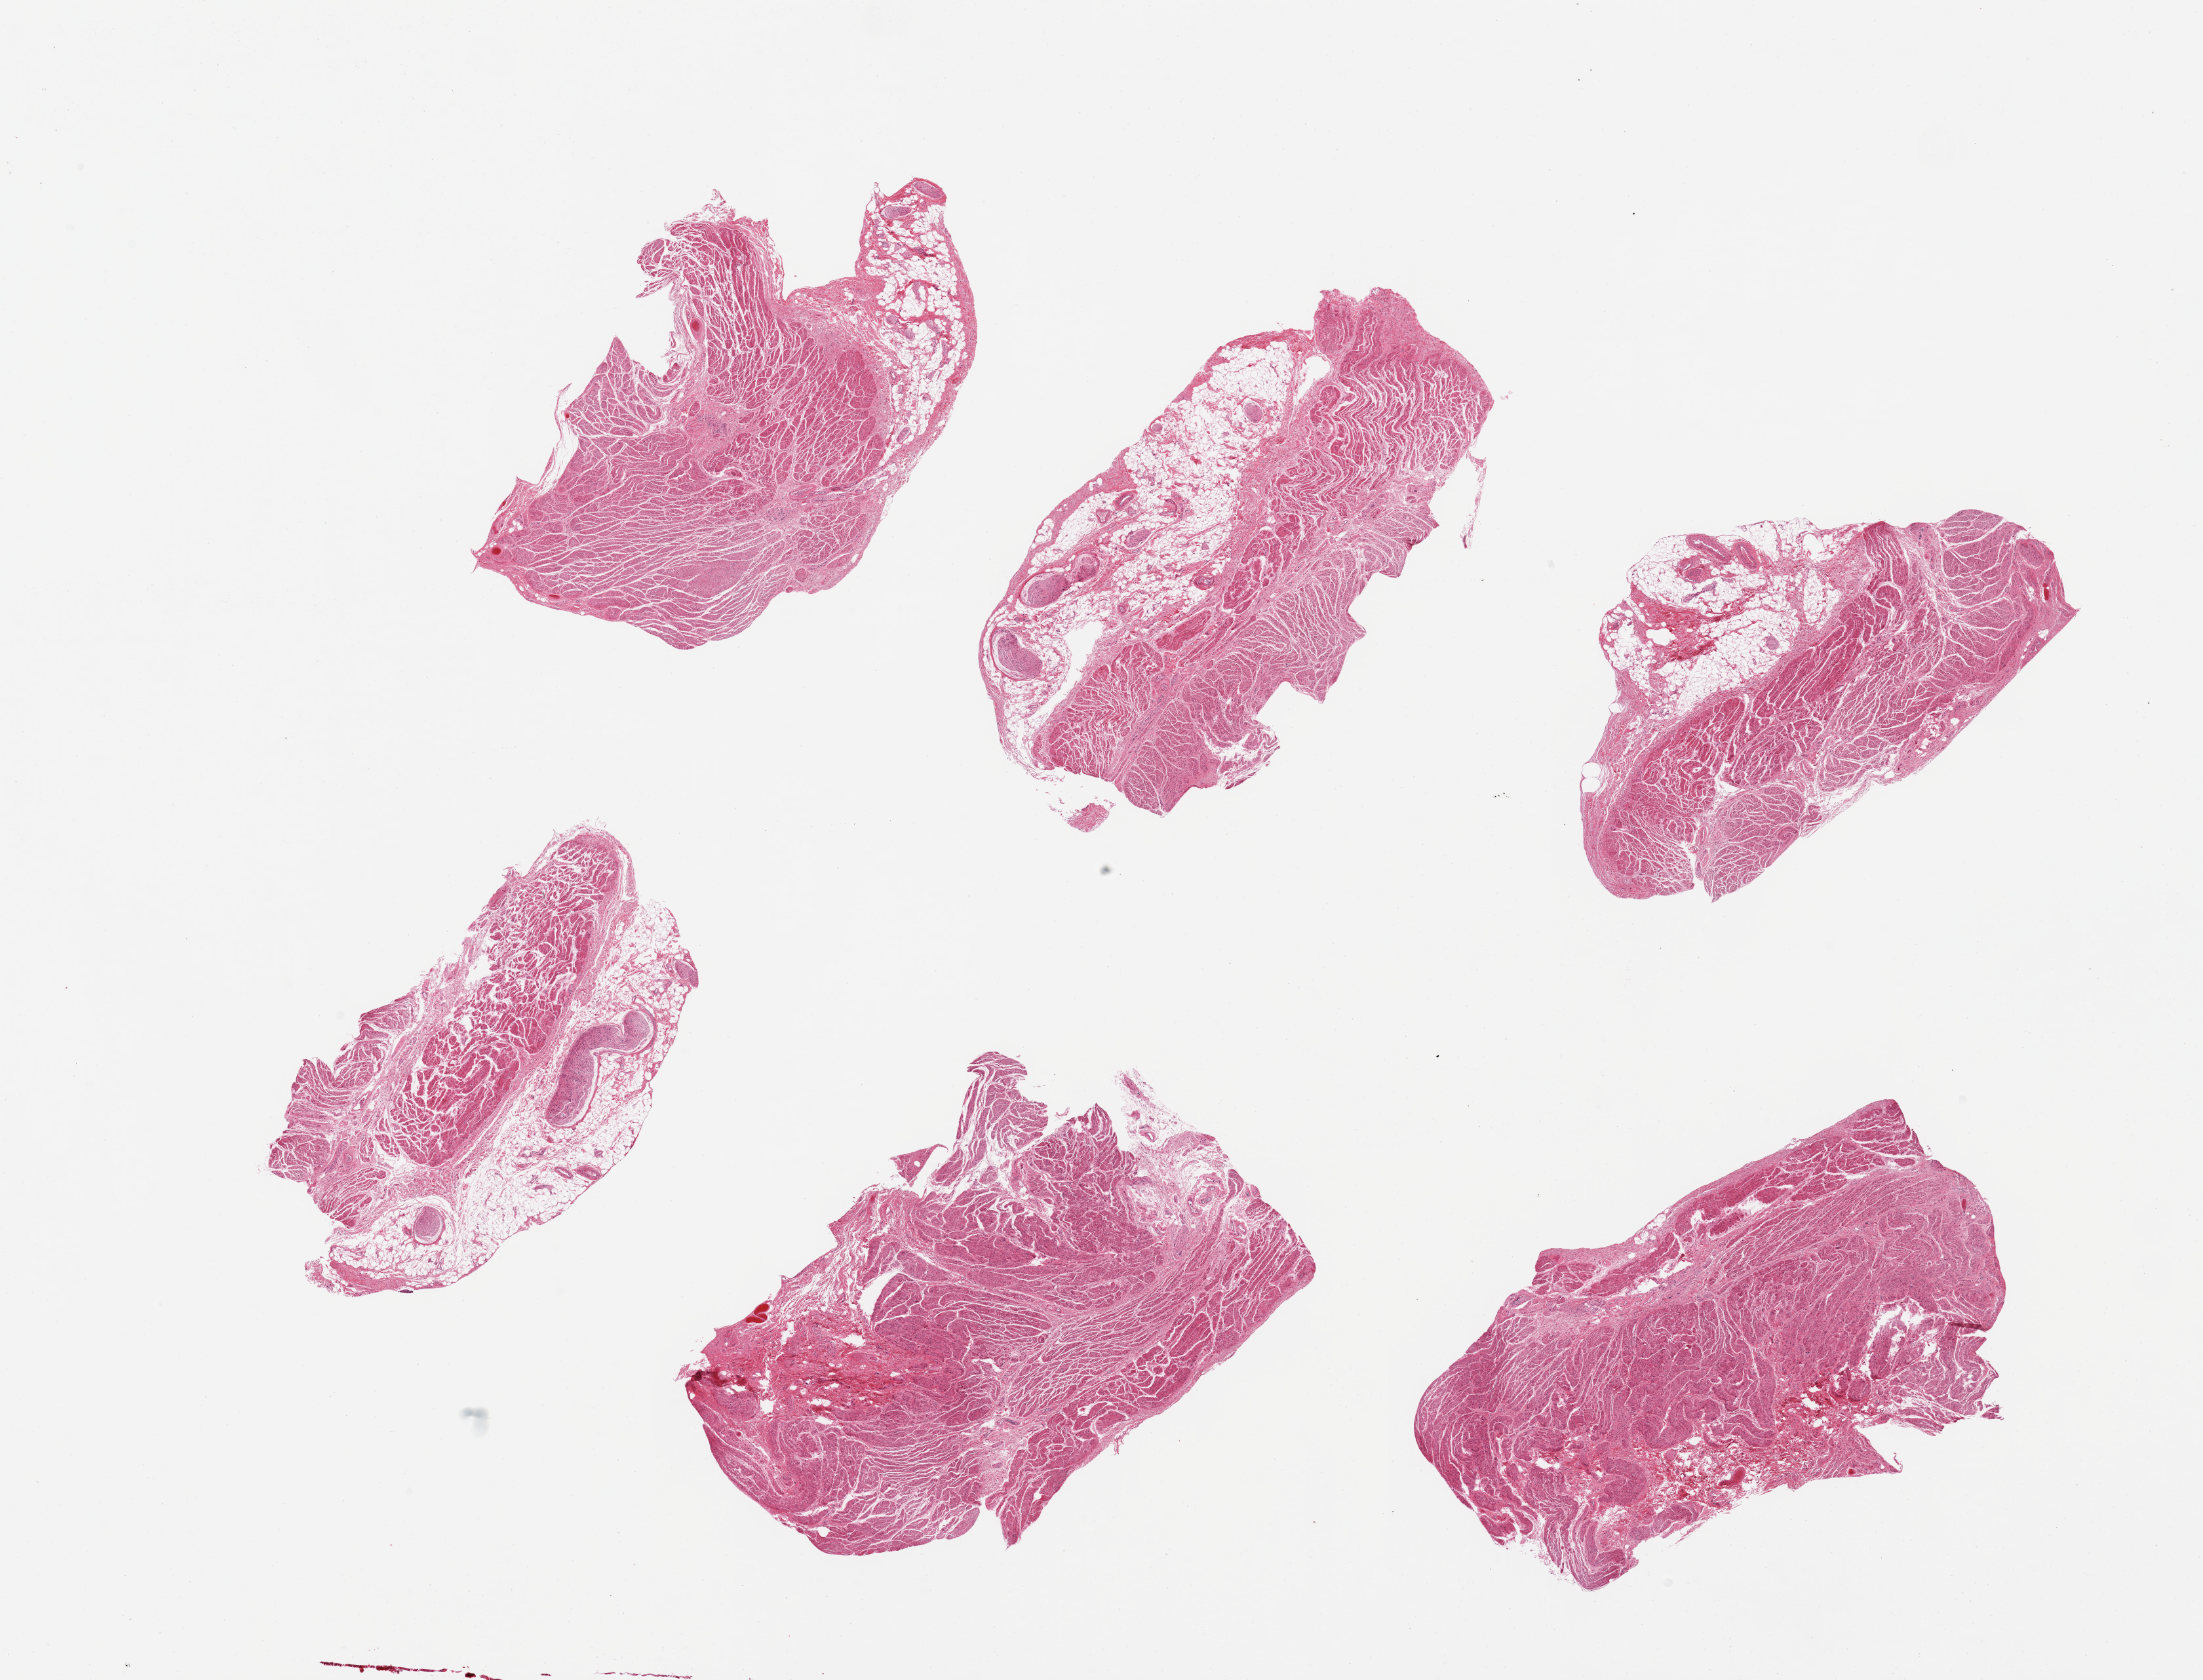
Hematoxylin and eosin (H&E) whole-slide image — whole scanned area (about 26.6 x 20.3 mm) shown as a low-resolution overview; PAXgene-fixed paraffin-embedded (PFPE) section; section of gastroesophageal junction (target tissue); donor tissue sample.
• review note (as recorded): 6 pieces, most with adherent fat/serosa